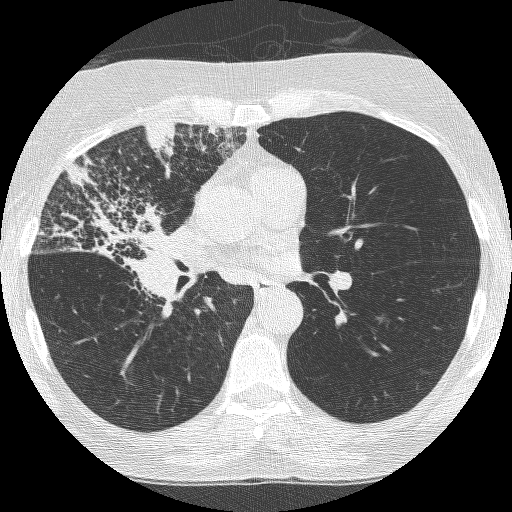
Axial slice from a low-dose chest CT screening exam; third screening round (two years after baseline); lung window (W 1500 / L -600 HU); lung (sharp) reconstruction kernel (BONE); slice 141 of 253 in the series; 512 × 512 image matrix, field of view 294 × 294 mm. Female participant, aged 64 years at enrolment. Former smoker at enrolment.
• Lesion marked by an expert reader, box from (x=63, y=174) to (x=201, y=314) px.
• The exam's reader record, not a measurement of the box and not confirmed to be the same lesion: non-calcified nodule or mass ≥4 mm, right upper lobe, 49 × 43 mm, spiculated (stellate) margins, soft tissue attenuation, pre-existing on the prior screen: yes; interval growth: yes.
• Participant outcome: lung cancer diagnosed 7 days after this screen — adenocarcinoma, NOS, right upper lobe, right middle lobe, right hilum, stage IV (AJCC 6th edition), 85 mm at pathology.